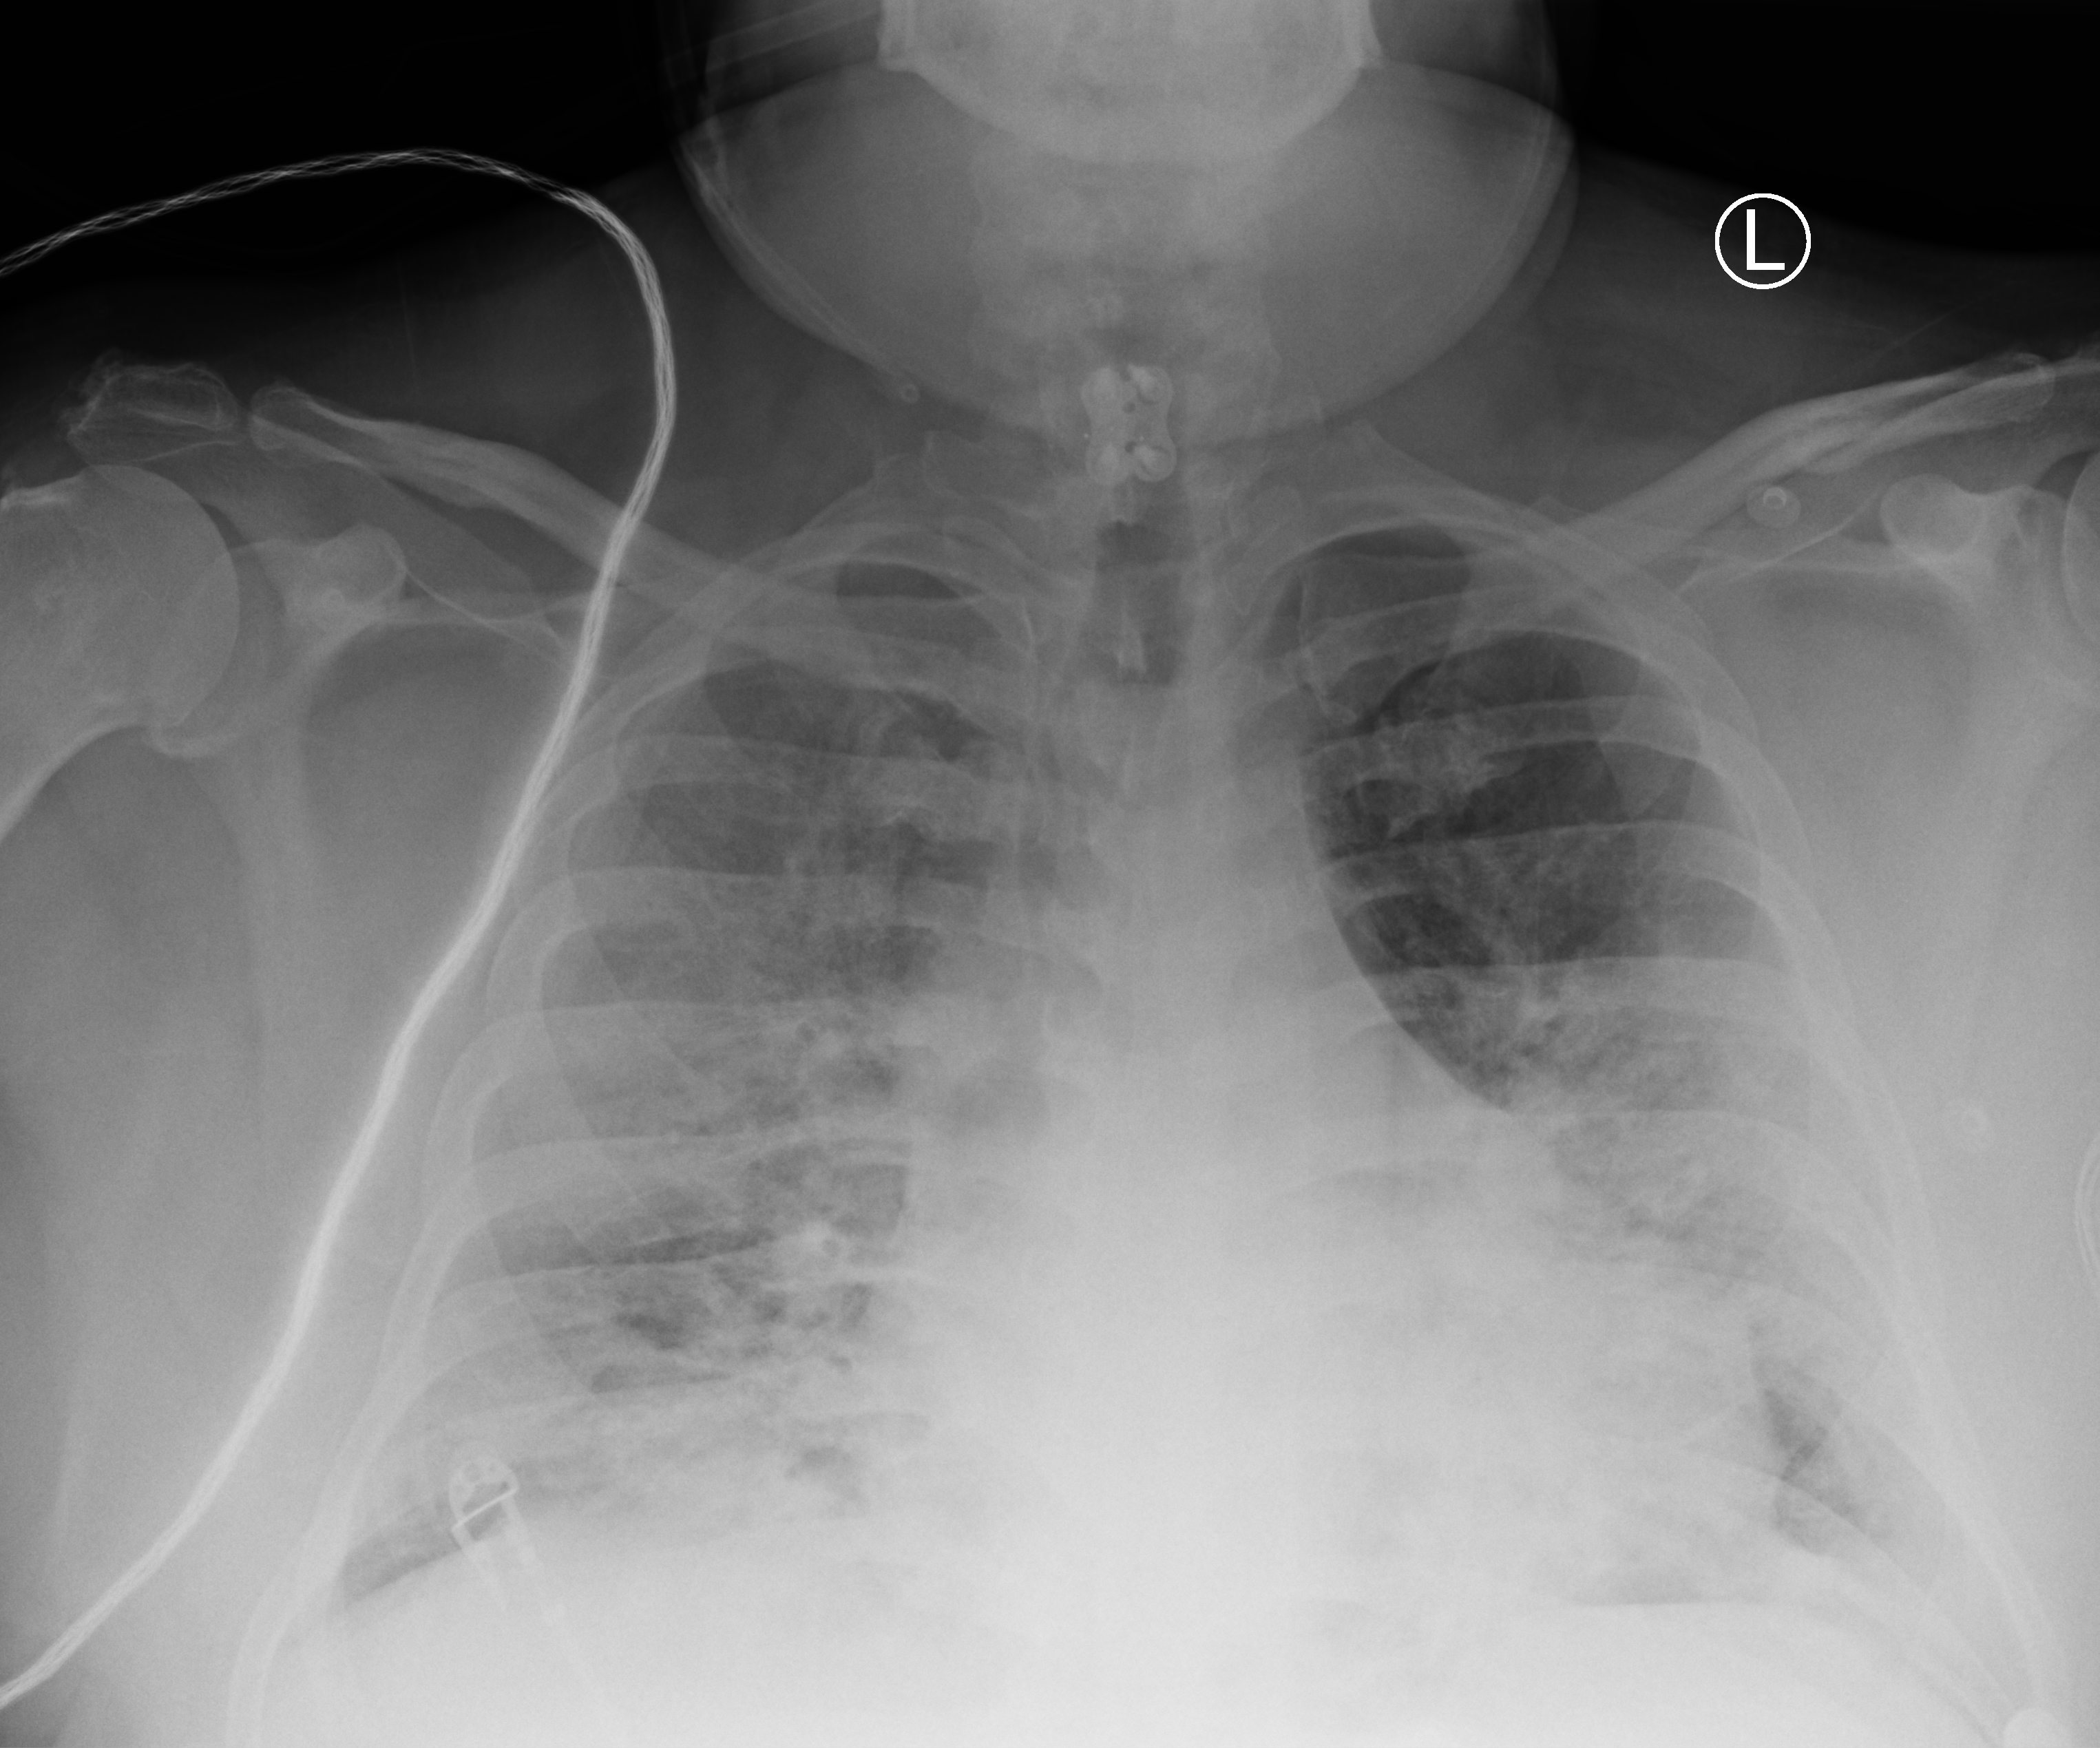
Chest X-ray (portable). Patient hospitalised with COVID-19; male, aged 18–59 years.
From the hospital-stay record, not from the radiograph (when in the stay this image was taken is not recorded): mechanically ventilated during this hospital stay: yes; admitted to intensive care during this hospital stay: yes; COPD (admission record): no.